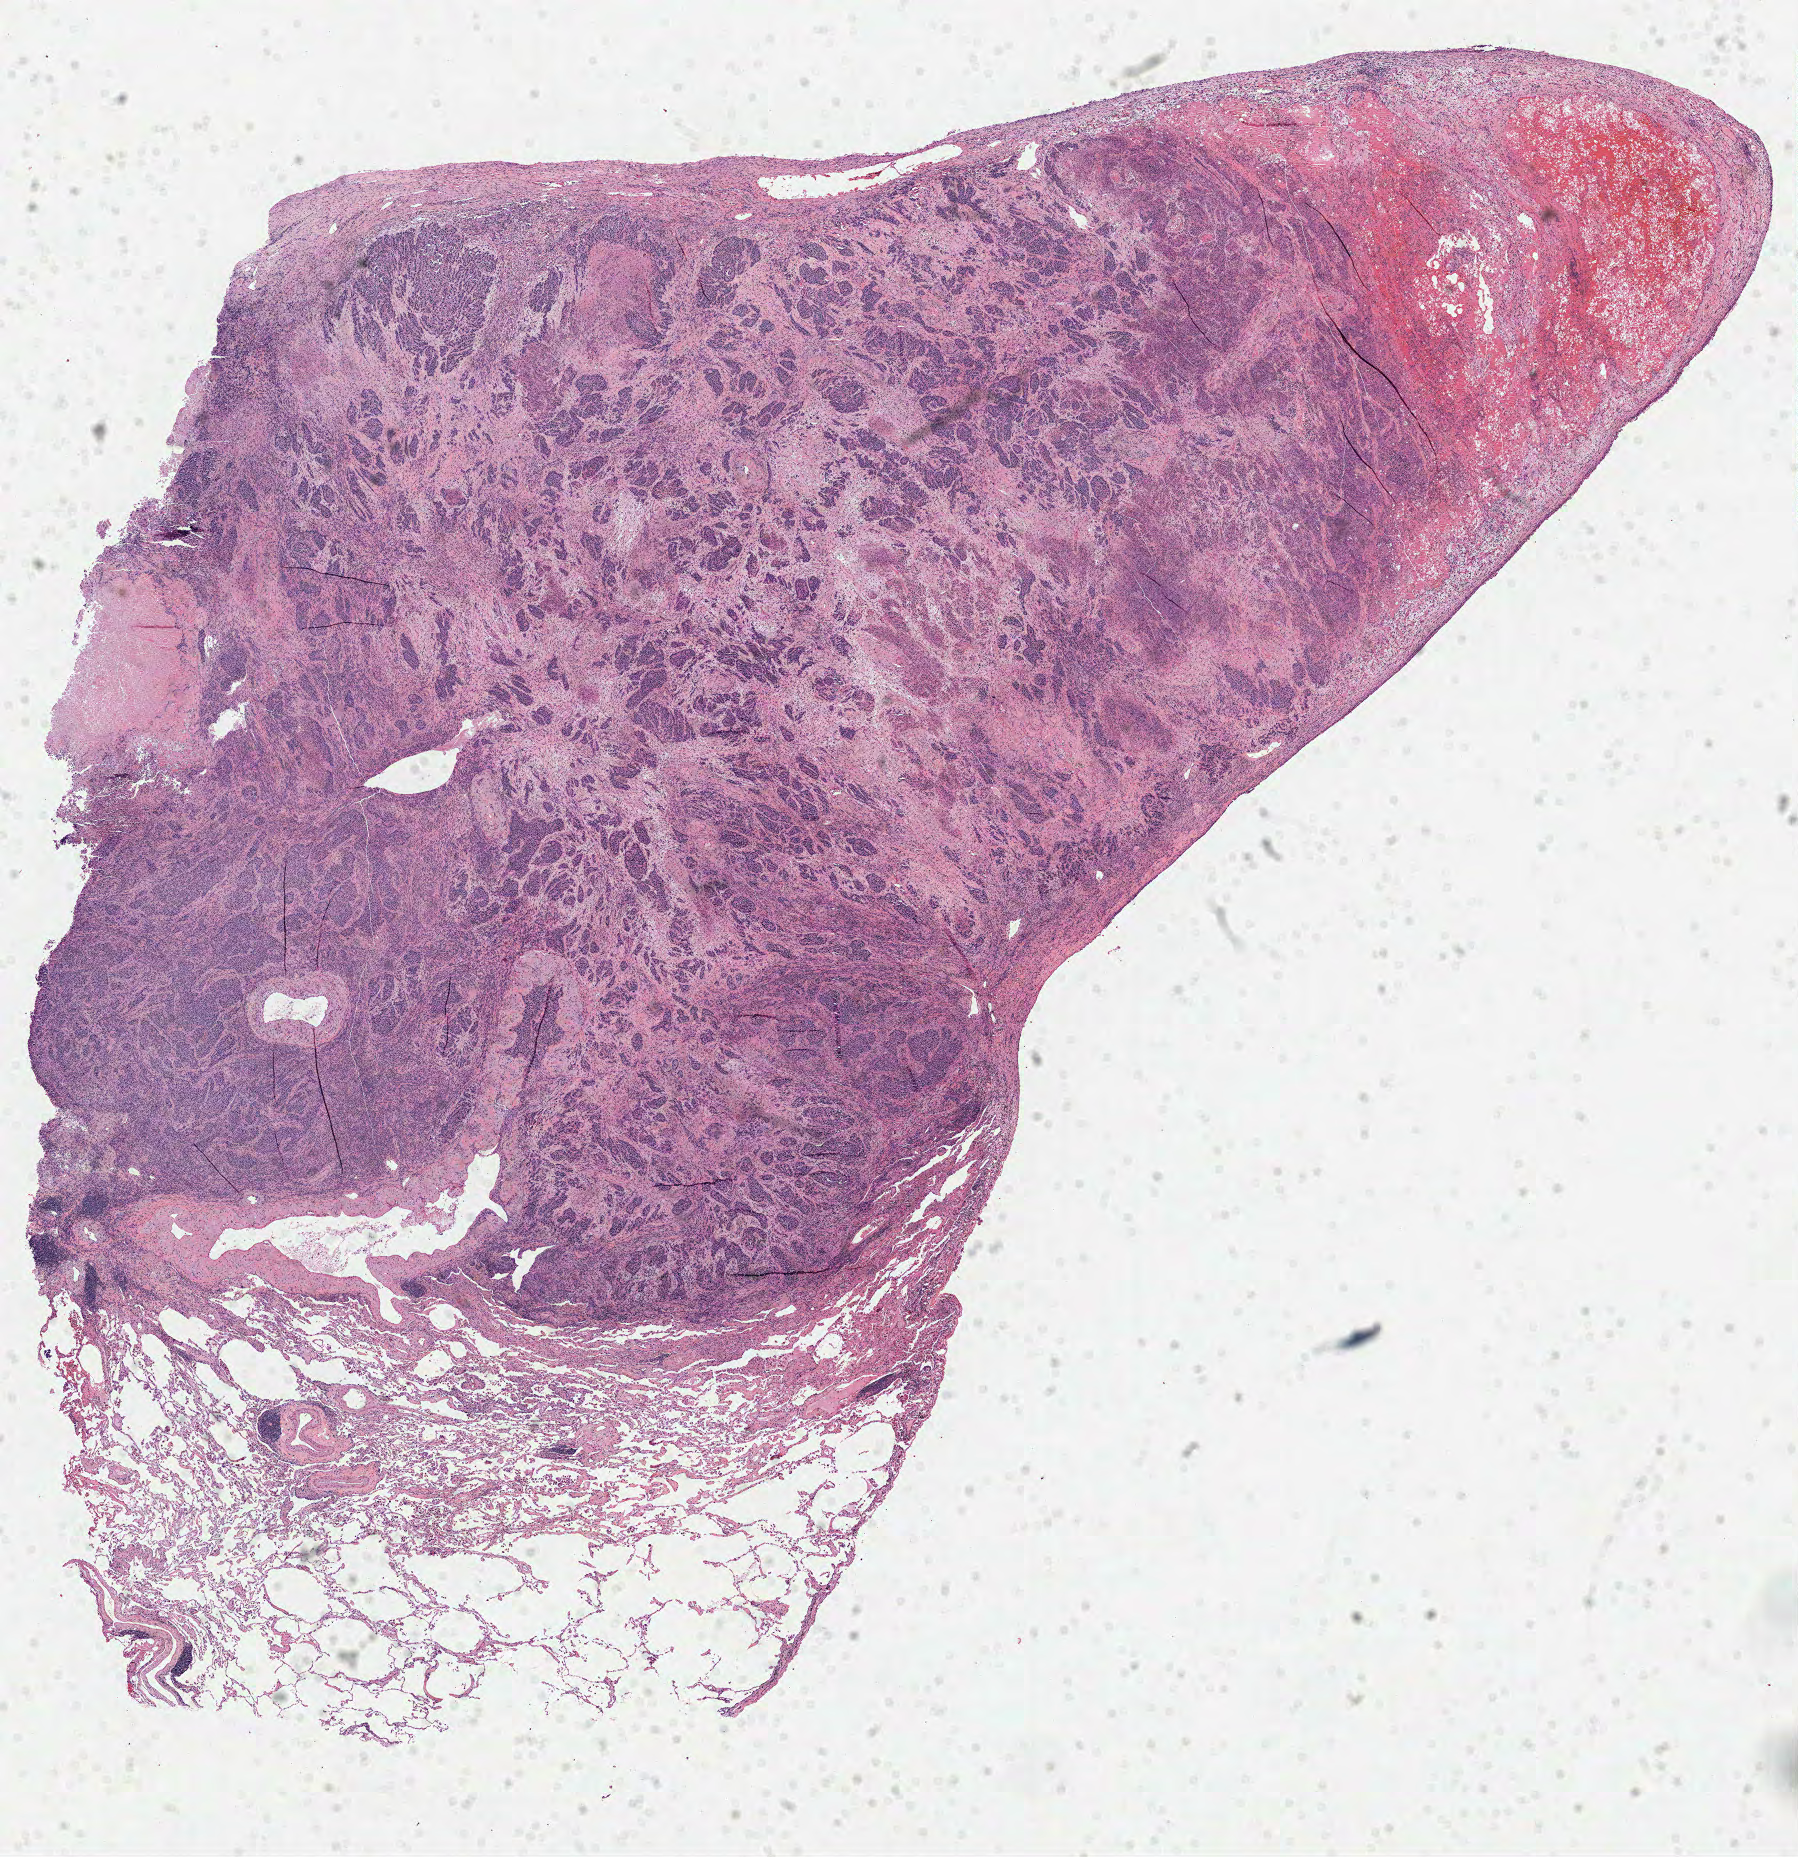
Whole-slide histology image, Hematoxylin and eosin (H&E) stained — a low-resolution overview of the entire scanned area, about 14.5 x 15.0 mm (acquisition: 40x scan), formalin-fixed paraffin-embedded (FFPE) diagnostic section, primary tumour sample from the lung. Male patient; age at initial diagnosis 61 years.
Histologic diagnosis: Adenocarcinoma, NOS (lower lobe, lung).